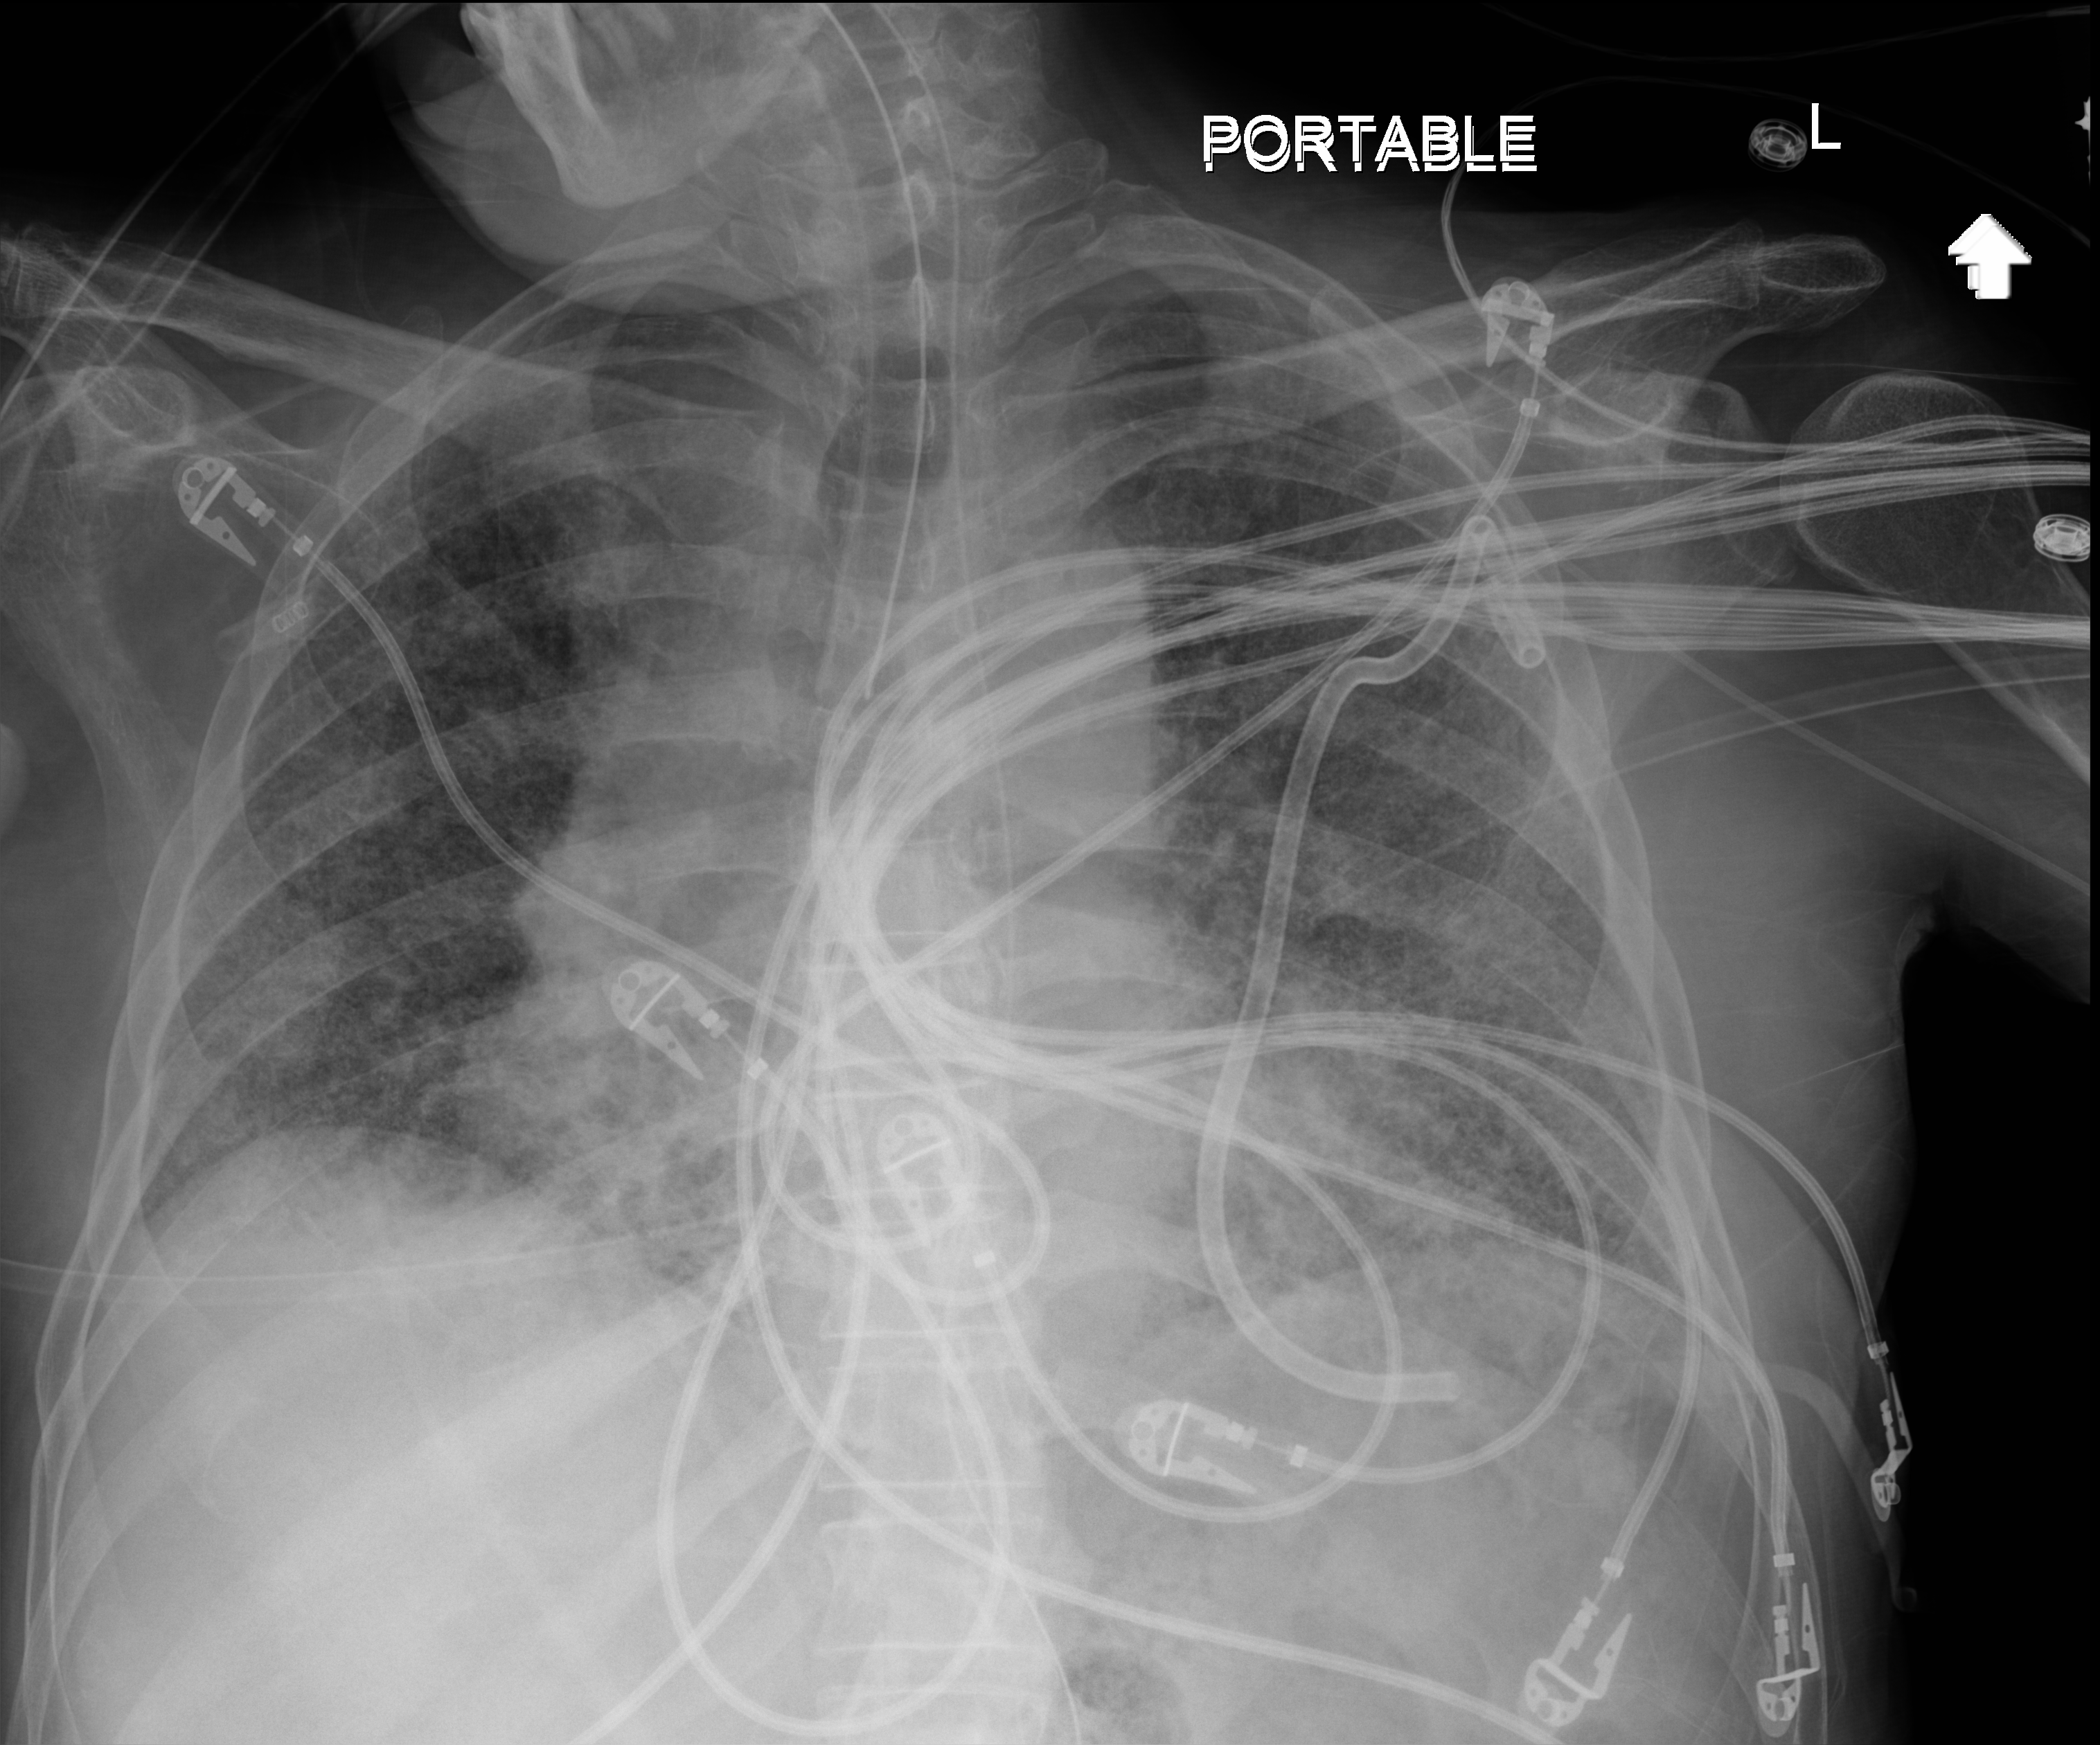
Chest X-ray; anteroposterior (AP) projection. Male patient hospitalised with COVID-19, age 60–74 years.
From the hospital-stay record, not from the radiograph (when in the stay this image was taken is not recorded):
- admitted to intensive care during this hospital stay: yes
- mechanically ventilated during this hospital stay: yes